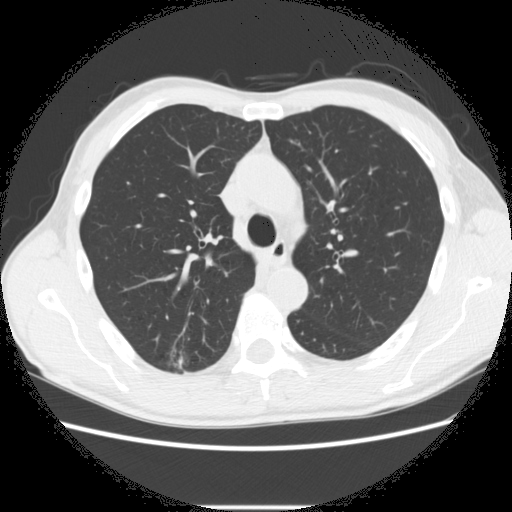
Low-dose screening chest CT, one axial slice. Position 196 of 282 along the scan axis. Reconstruction kernel STANDARD. Lung window (W 1500 / L -600 HU). 2.5 mm slice thickness. 512 × 512 image matrix, field of view 360 × 360 mm.
Annotated regions visible in this slice (outlined manually by an expert reader):
- lesion 1 (tumor, upper lobe of right lung): bounding box <175,357,184,369> (left, top, right, bottom; pixels)